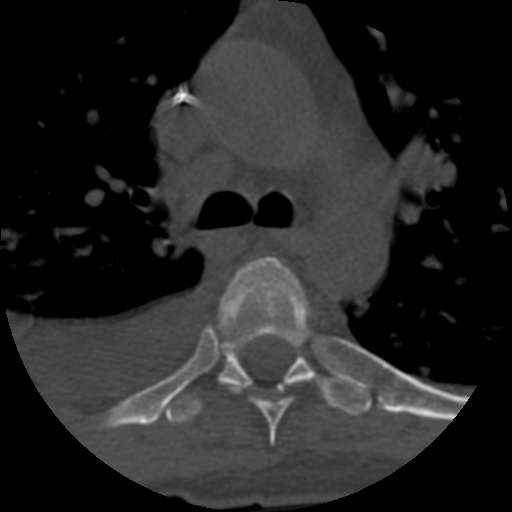
CT including the spine, one axial slice; position 445 of 708 along the scan axis; one of 3 acquisitions stored at this slice position; bone window (W 1800 / L 400 HU); 1.25 mm slice thickness; 512 × 512 image matrix, field of view 160 × 160 mm. Patient age 55 years. Case-level facts recorded for this patient, not image findings: primary cancer: colon; vertebrae with lytic lesions (as recorded): T12, L1, L5.
Outlined on this slice (semi-automatic segmentation, software-assisted and operator-edited):
- T5 vertebra: bounding box [x1, y1, x2, y2] px = [219, 256, 309, 445]
- T6 vertebra: [163, 333, 372, 424]